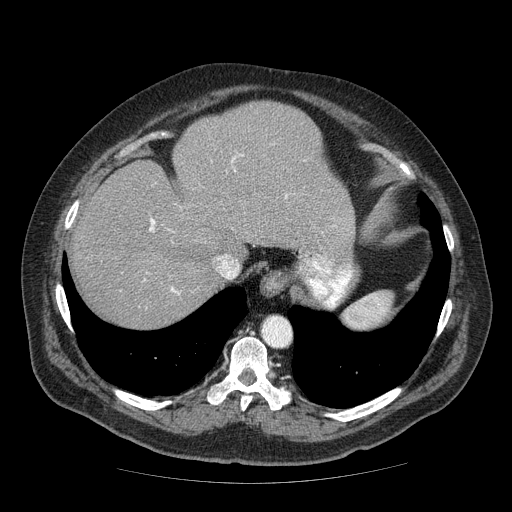
Contrast-enhanced abdominal CT (liver protocol), one axial slice; position 54 of 85 along the scan axis; reconstruction kernel STANDARD; 120 kVp; soft-tissue window (W 400 / L 40 HU); 2.5 mm slice thickness; 512 × 512 image matrix, field of view 420 × 420 mm. Case-level facts recorded for this patient, not image findings: diagnosis: hepatocellular carcinoma (patient treated with transarterial chemoembolisation; whether this scan precedes or follows treatment is not stated here); TNM stage (as recorded): Stage-IIIA; Child-Pugh class: A.
Outlined on this slice (semi-automatically segmented with operator editing):
- abdominal aorta: bounding box (x1, y1, x2, y2) in pixels: (262, 318, 291, 348)
- liver parenchyma outside the tumour (the mass and vessels are separate outlines, so this box may not span the whole liver): (70, 102, 354, 328)
- liver vessels: (149, 154, 288, 294)